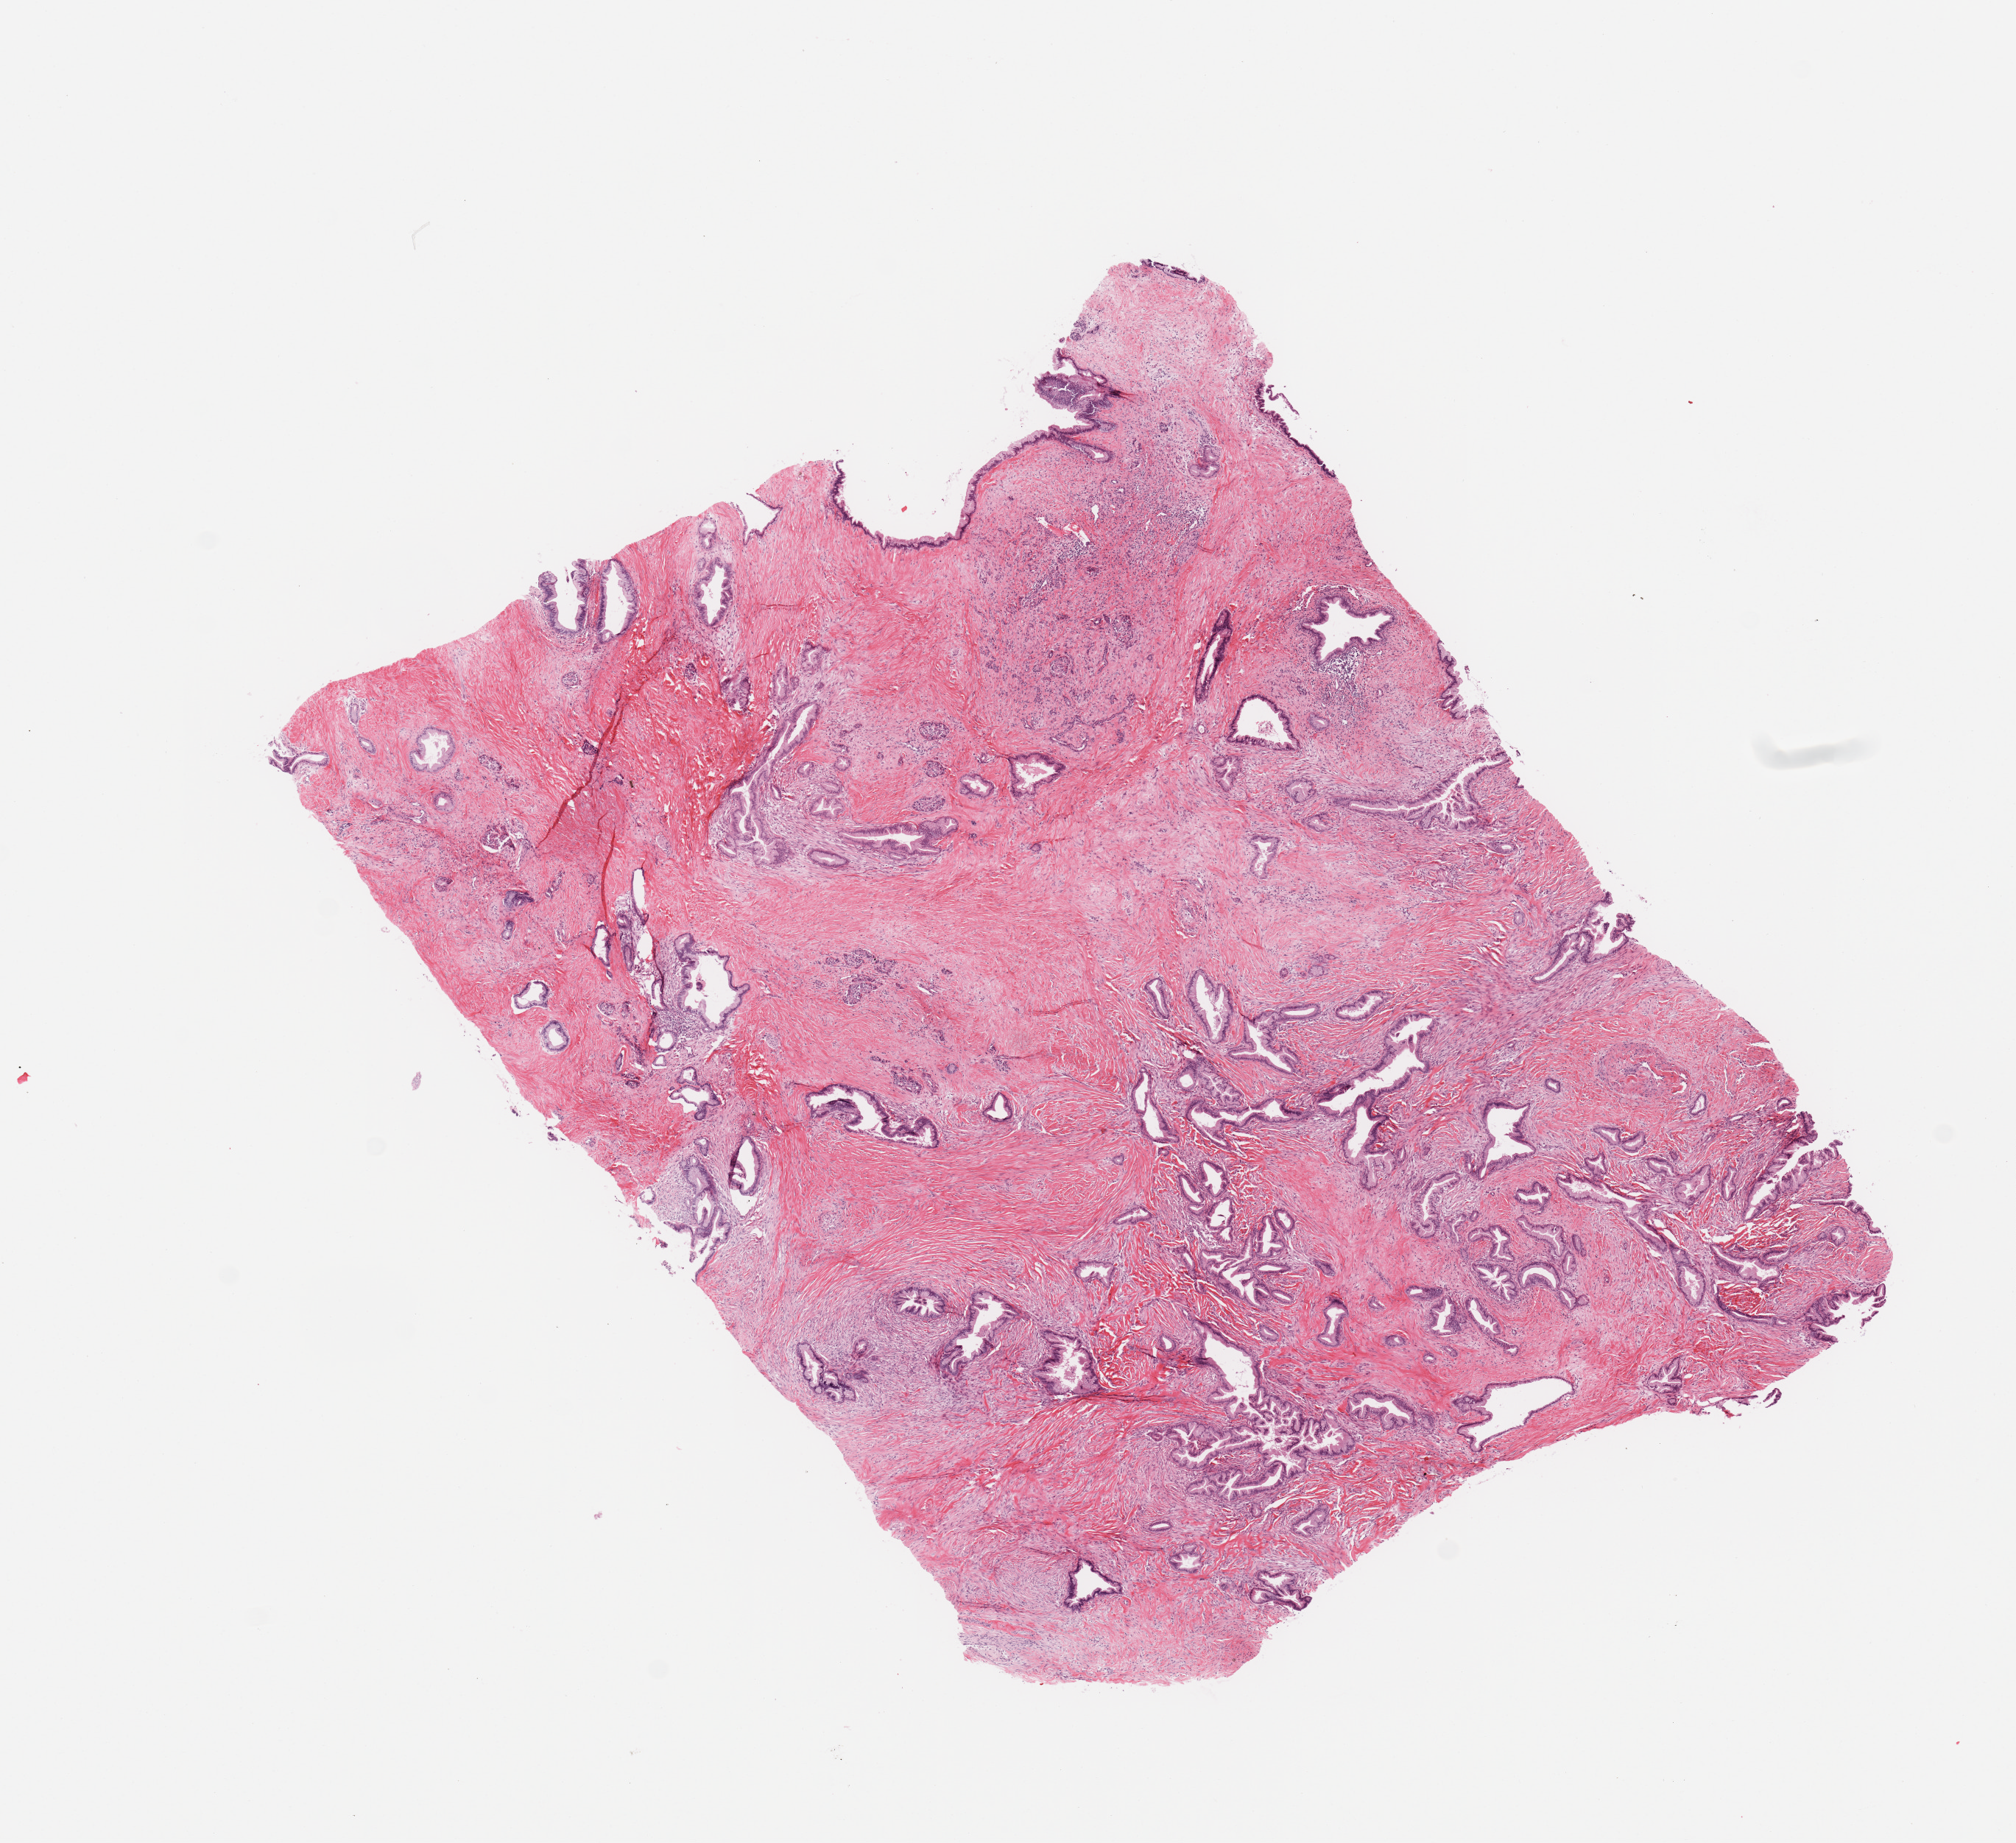
H&E-stained whole-slide image, whole scanned area (about 10.8 x 9.9 mm, from a 20x scan) shown as a low-resolution overview, tumour tissue sample, pancreas. 69-year-old male patient. Histologic grade: G2 (moderately differentiated).
* primary tumour site (as recorded): body
* AJCC pathologic stage: IIB
* histologic diagnosis: Infiltrating duct carcinoma, NOS